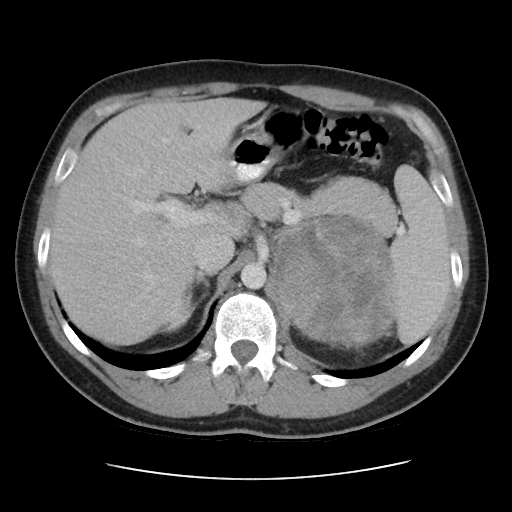
Contrast-enhanced abdominal CT, one axial slice; slice 30 of 48 in the series (ordered by position); 120 kVp; soft-tissue window (W 400 / L 40 HU); 512 × 512 image matrix, field of view 360 × 360 mm. Male patient, age 32 years. Case-level facts recorded for this patient, not image findings: diagnosis: adrenocortical carcinoma; tumour side: left adrenal; tumour size at pathology: 14 cm; Ki-67 index: 67 %; stage (as recorded): 3.
Annotated regions visible in this slice (semi-automatically segmented with operator editing):
- mass: box from (x=278, y=219) to (x=395, y=345) px